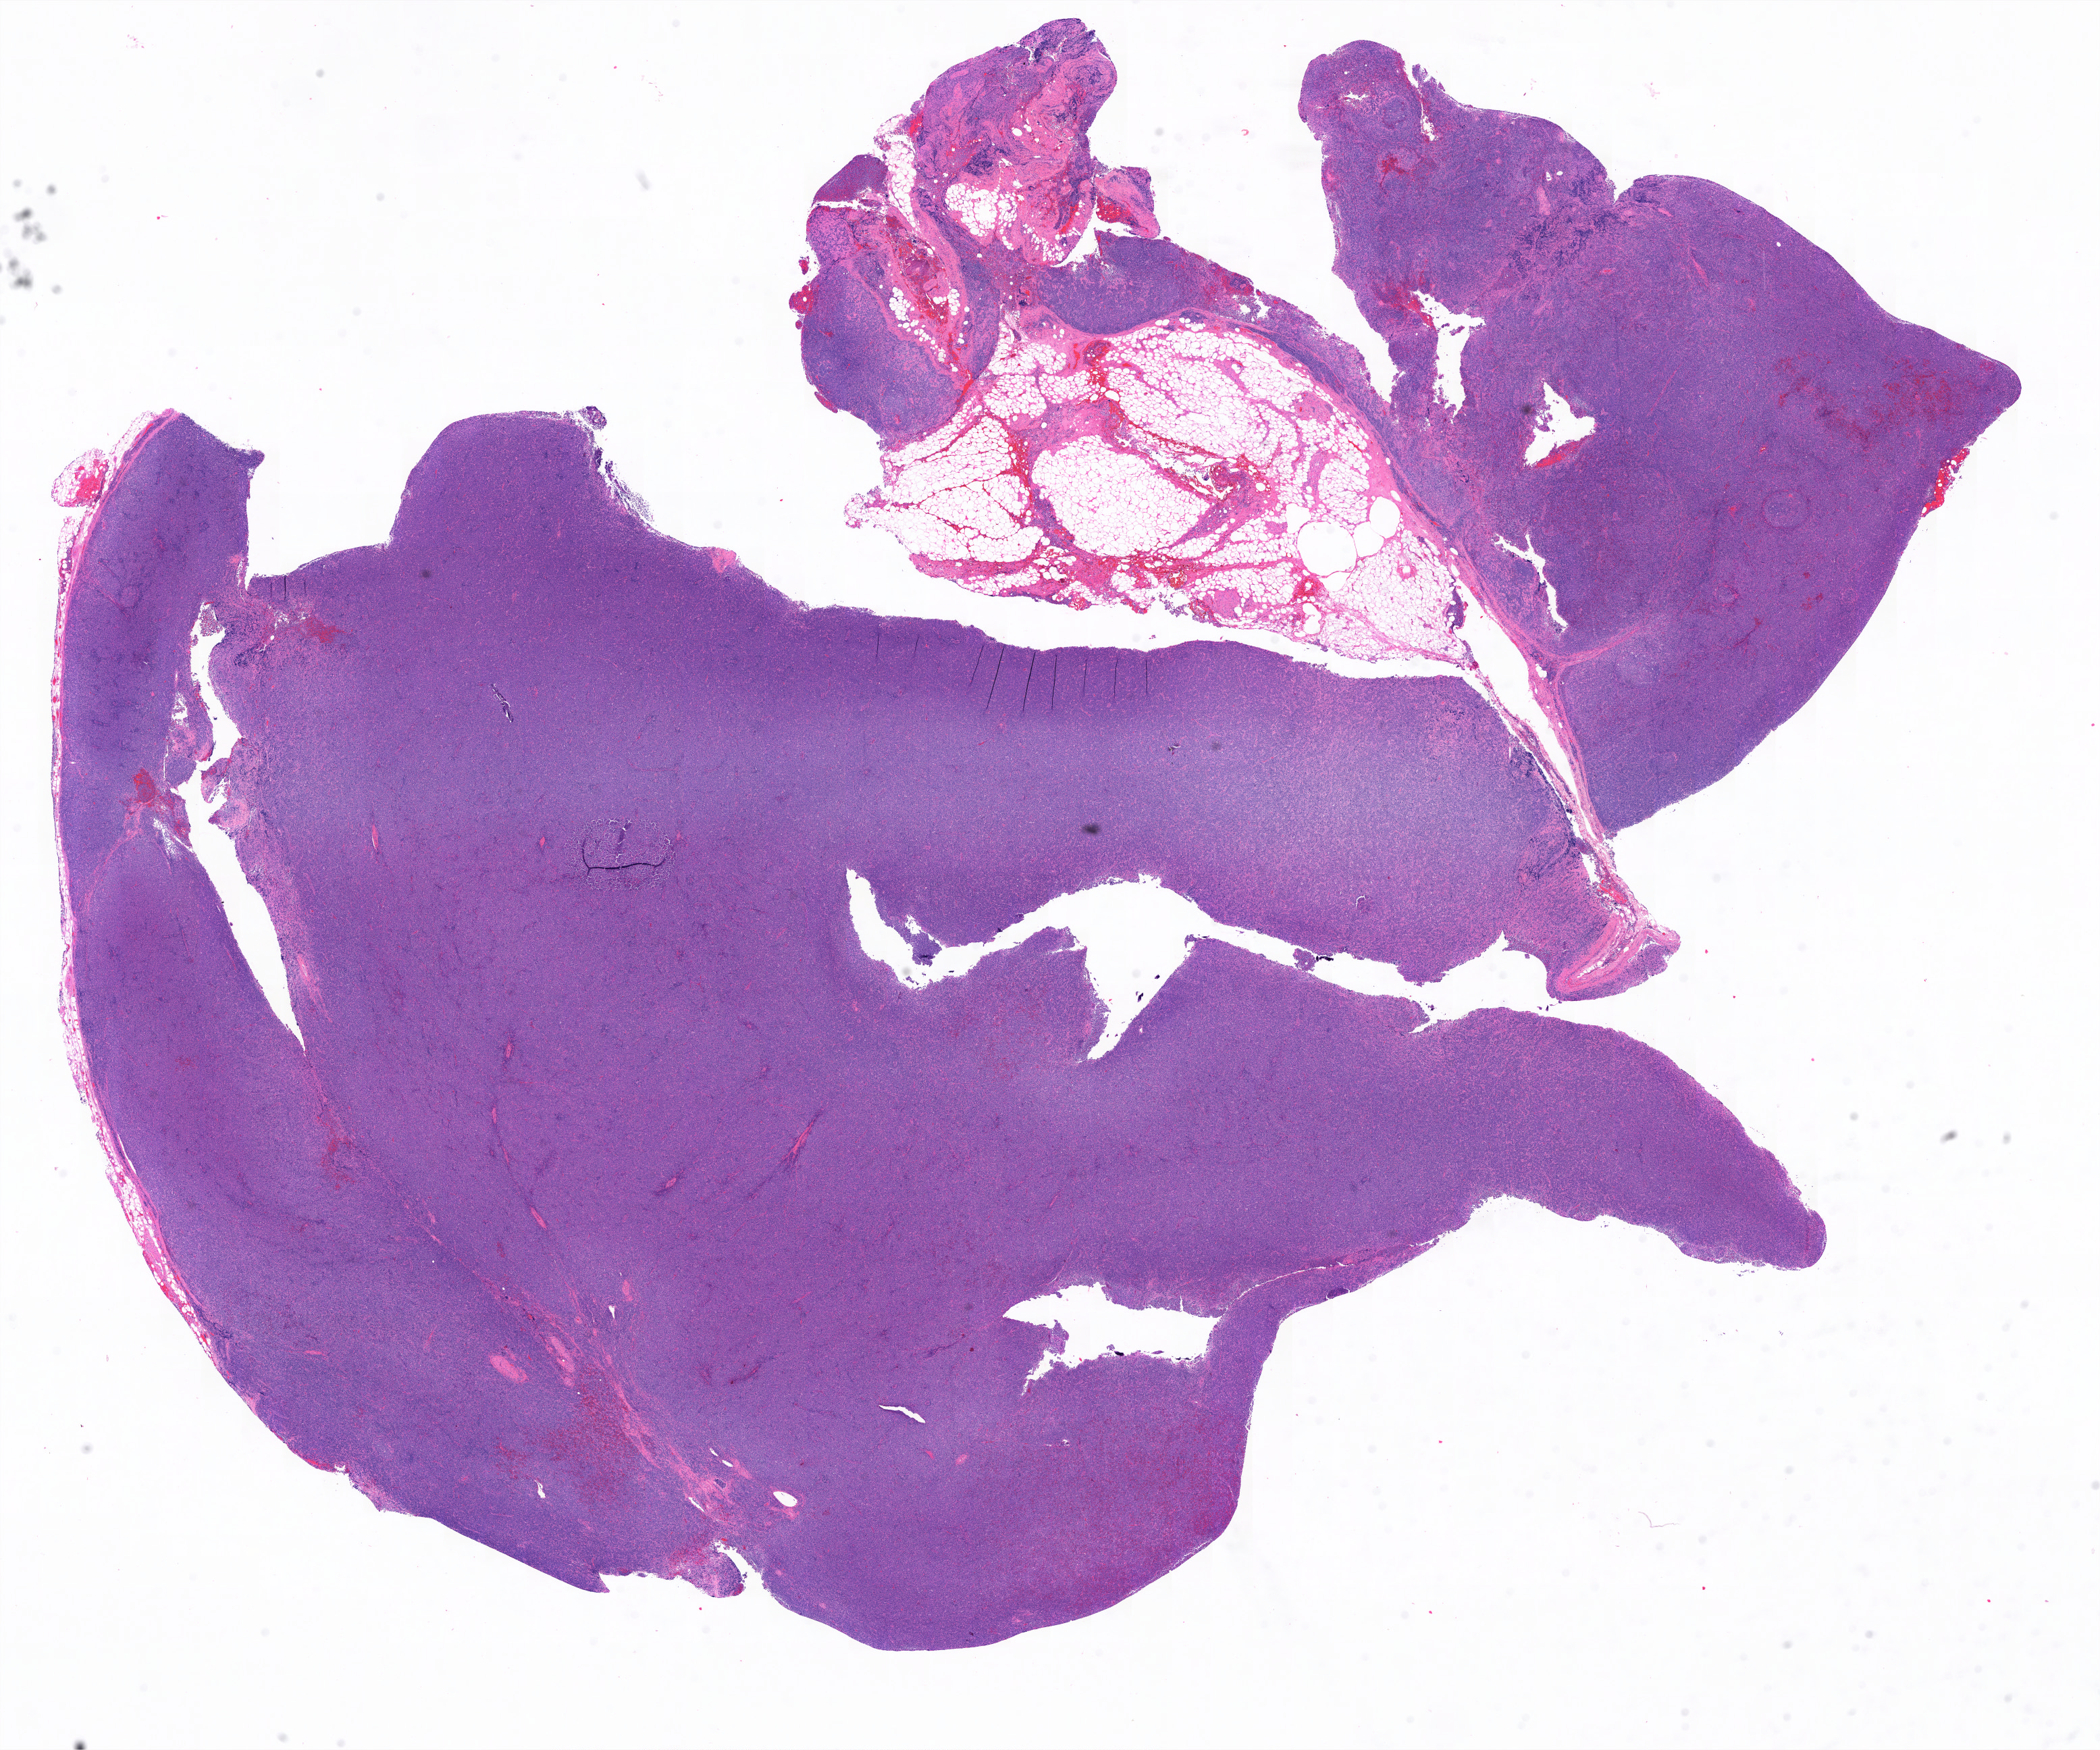
H&E whole-slide image — low-resolution overview of the scanned area, about 23.1 x 19.3 mm, formalin-fixed paraffin-embedded (FFPE) diagnostic section, primary tumour sample from the lymphoid tissue. Female, age 54 years at initial diagnosis.
* histologic diagnosis: Diffuse large B-cell lymphoma, NOS (lymph nodes of head, face and neck)